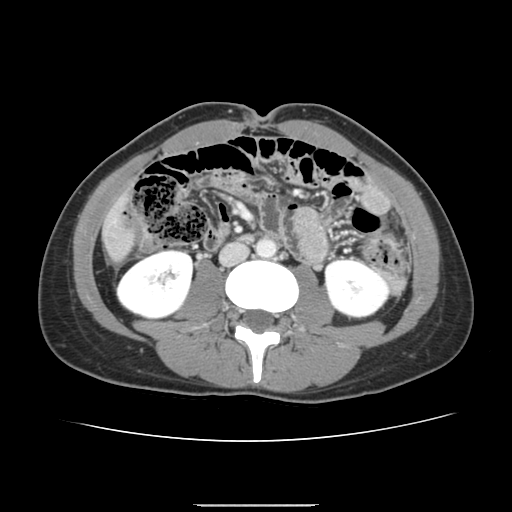
Contrast-enhanced abdominal CT, one axial slice; slice 37 of 150 in the series (ordered by position); 120 kVp; intravenous contrast given; soft-tissue window (W 400 / L 40 HU); 512 × 512 image matrix, field of view 324 × 324 mm. Female patient, age 32 years. From the clinical record (not read from this slice): diagnosis: colorectal cancer liver metastases, imaged before liver resection; multiple liver metastases: yes; largest metastasis: 0.7 cm; chemotherapy before resection: yes.
Structures marked on this image (manually delineated by an expert):
- liver: bounding box <105,205,131,259> (left, top, right, bottom; pixels)
- planned liver remnant (the part of the liver to remain after resection): <106,206,131,259>